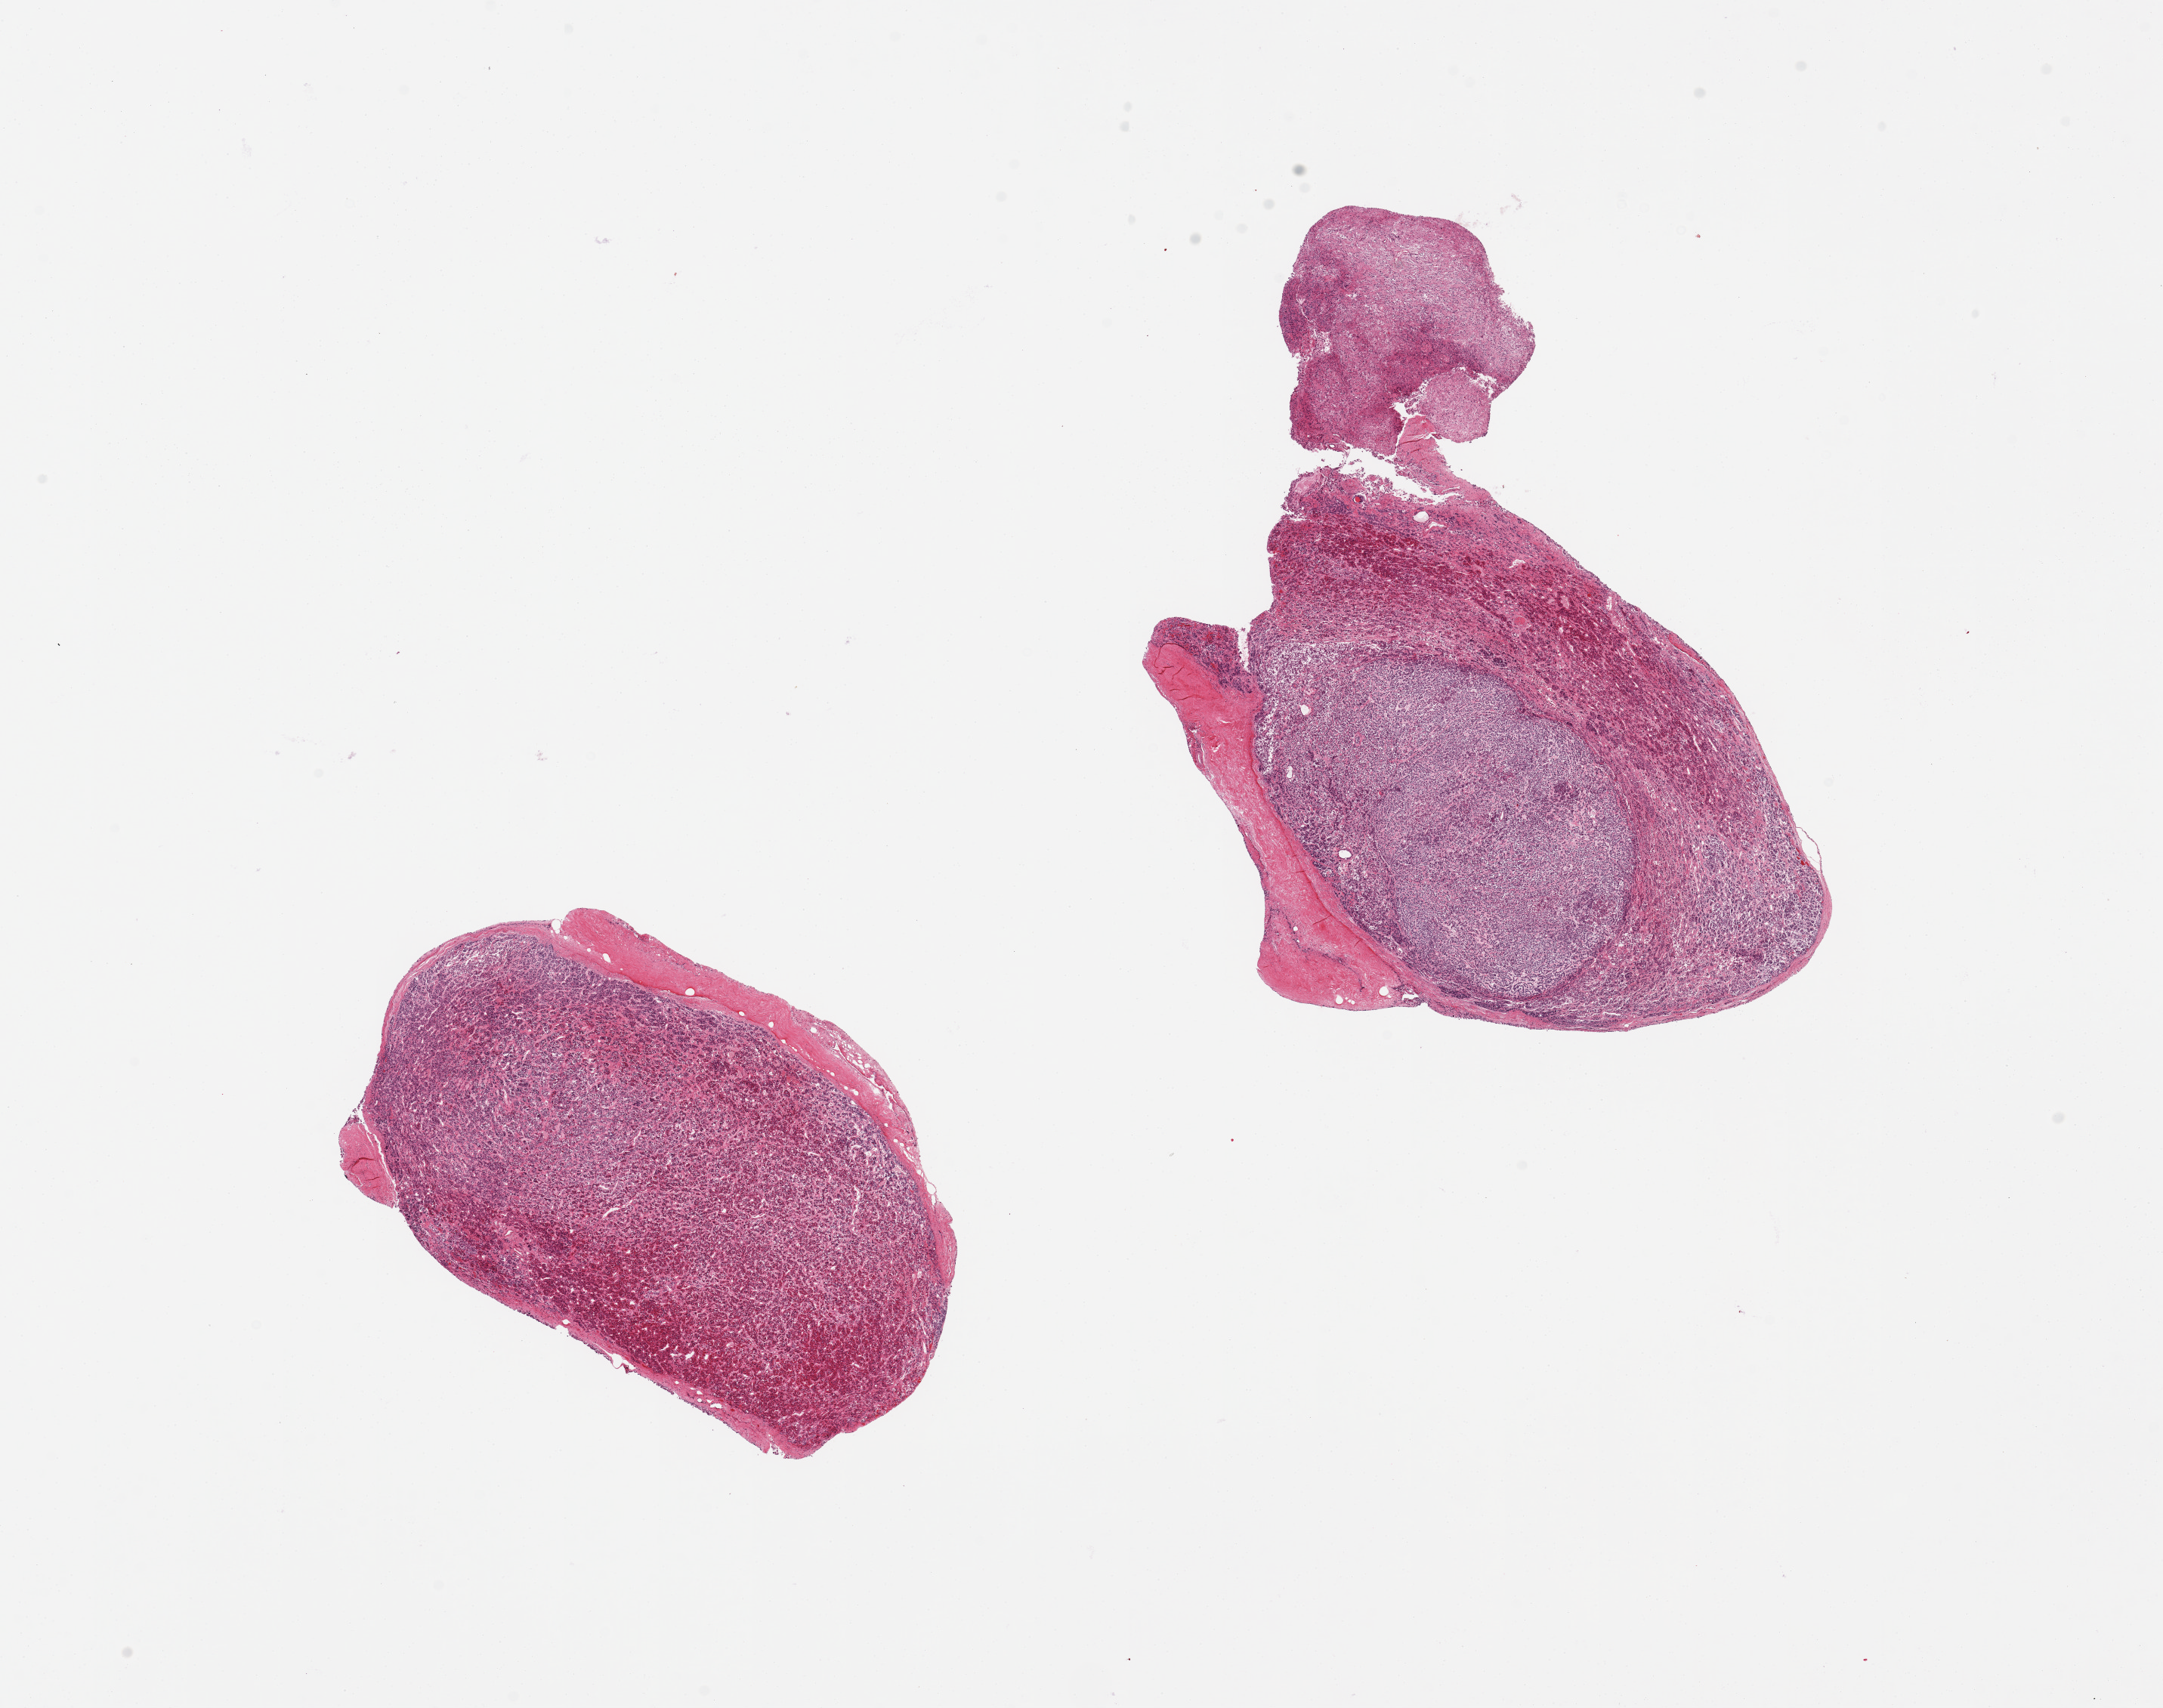
H&E whole-slide image — whole scanned area (about 22.6 x 17.9 mm, slide scanned at 20x) shown as a low-resolution overview, PAXgene-fixed, paraffin-embedded tissue, section of pituitary (target tissue), donor tissue sample. Donor sex: male.
Review note (as recorded): 2 pieces 9 x 5 and 7 x 4 mm. A 5 x 3 mm adenoma is present in 1 piece. A 2.5 mm piece of posterior pituitary is present at edge of one piece.